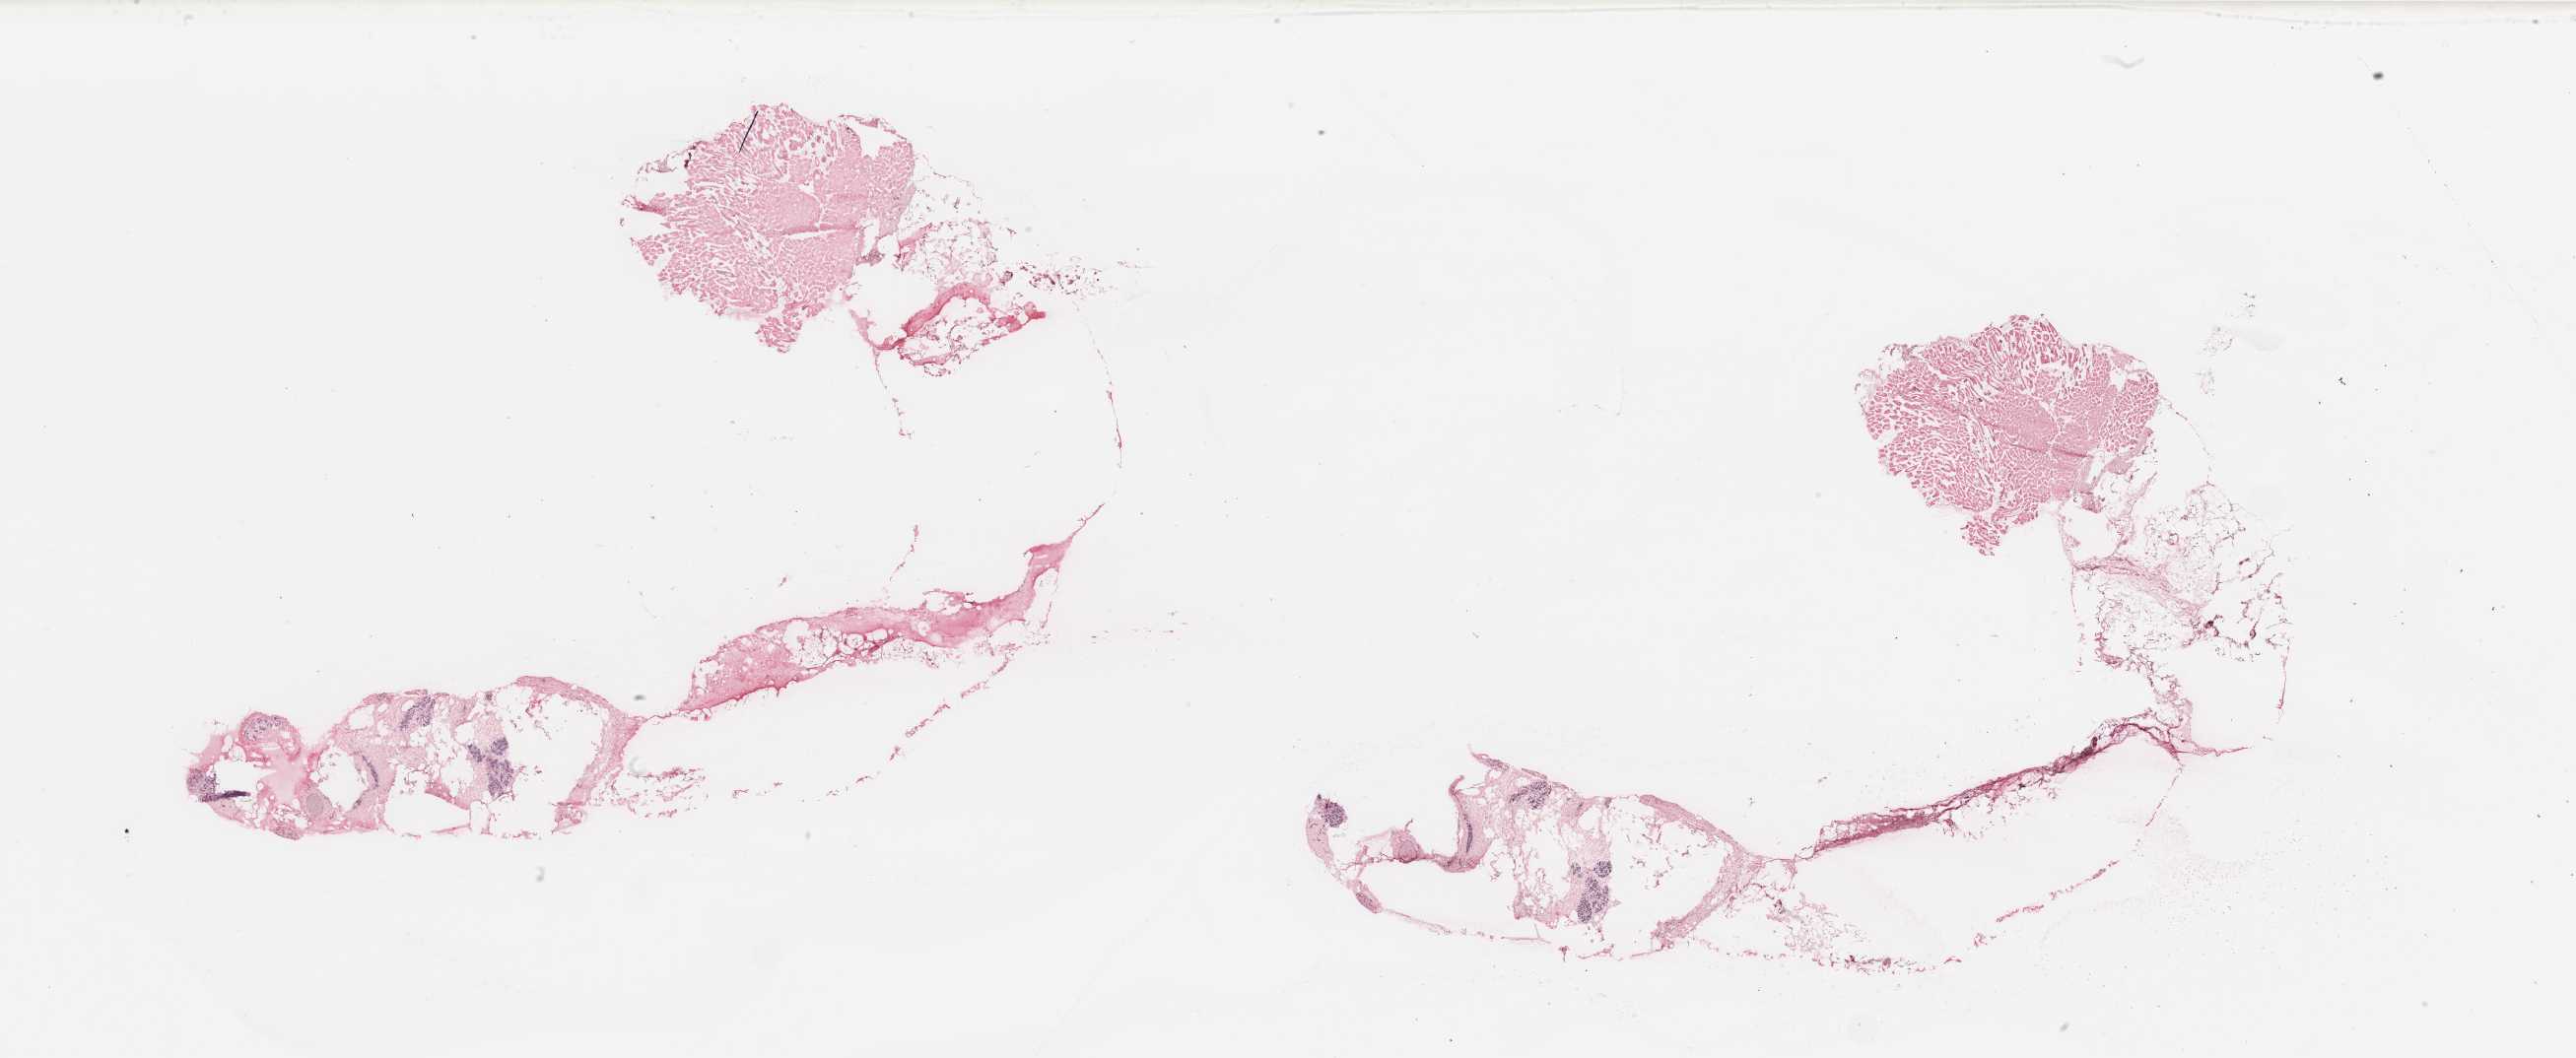
Whole-slide histology image, H&E-stained, low-resolution overview of the scanned area, about 41.3 x 17.0 mm. Breast, tissue type not recorded.
• patient diagnosis (cohort enrolment): breast cancer (breast)